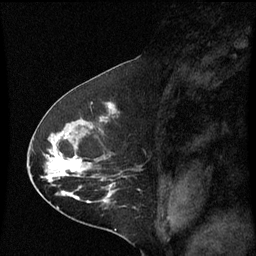
Breast MRI (dynamic contrast-enhanced), one sagittal slice; position 34 of 60 along the scan axis; dynamic contrast-enhanced series, image 2 of 3 at this slice position (ordered by acquisition); 1.5 T; TE 4.2 ms, TR 8.9 ms; 2 mm slice thickness; 256 × 256 image matrix, field of view 200 × 200 mm. Female patient, age 53 years. Case-level facts recorded for this patient, not image findings: setting: breast cancer imaged before/during neoadjuvant chemotherapy; receptor status: HR-positive, HER2-negative.
Outlined on this slice (semi-automatic segmentation, software-assisted and operator-edited):
- analysis volume of interest (the breast-tissue region the enhancement analysis was run in; not a lesion): bounding box [x1, y1, x2, y2] px = [32, 100, 125, 221]
- tumour enhancement mask (voxels above the 70 % enhancement threshold inside the analysis volume of interest): [46, 154, 111, 203]